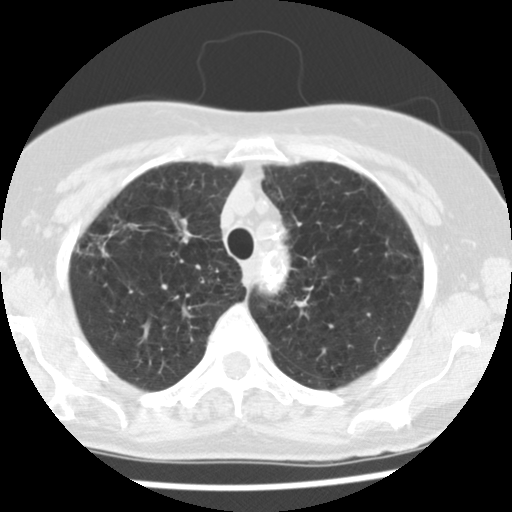
Chest CT (low-dose screening protocol), one axial image. First (baseline) screen. Lung window (W 1500 / L -600 HU). 2.5 mm slice thickness. Slice 26 of 121 in the series. 512 × 512 image matrix, field of view 290 × 290 mm. Female participant, aged 70 years at enrolment. Former smoker at enrolment.
• Expert reader's lesion annotation, bounding box (x1, y1, x2, y2) in pixels: (151, 202, 213, 259).
• Screening reader's record for this exam (one nodule recorded; not confirmed to be the boxed lesion): non-calcified nodule or mass ≥4 mm, left upper lobe, 8 × 6 mm, poorly defined margins, soft tissue attenuation.
• Note: the box lies in the patient's right hemithorax on this image, whereas the reader's record names the left lung; they may be different findings.
• Official screen result: positive, change unspecified: nodule(s) >= 4 mm or enlarging nodule(s), mass(es), or other non-specific abnormalities suspicious for lung cancer.
• Lung cancer was diagnosed 745 days after this screen (after the second annual screen): non-small cell carcinoma, right upper lobe, stage IV (AJCC 6th edition), 30 mm at pathology.